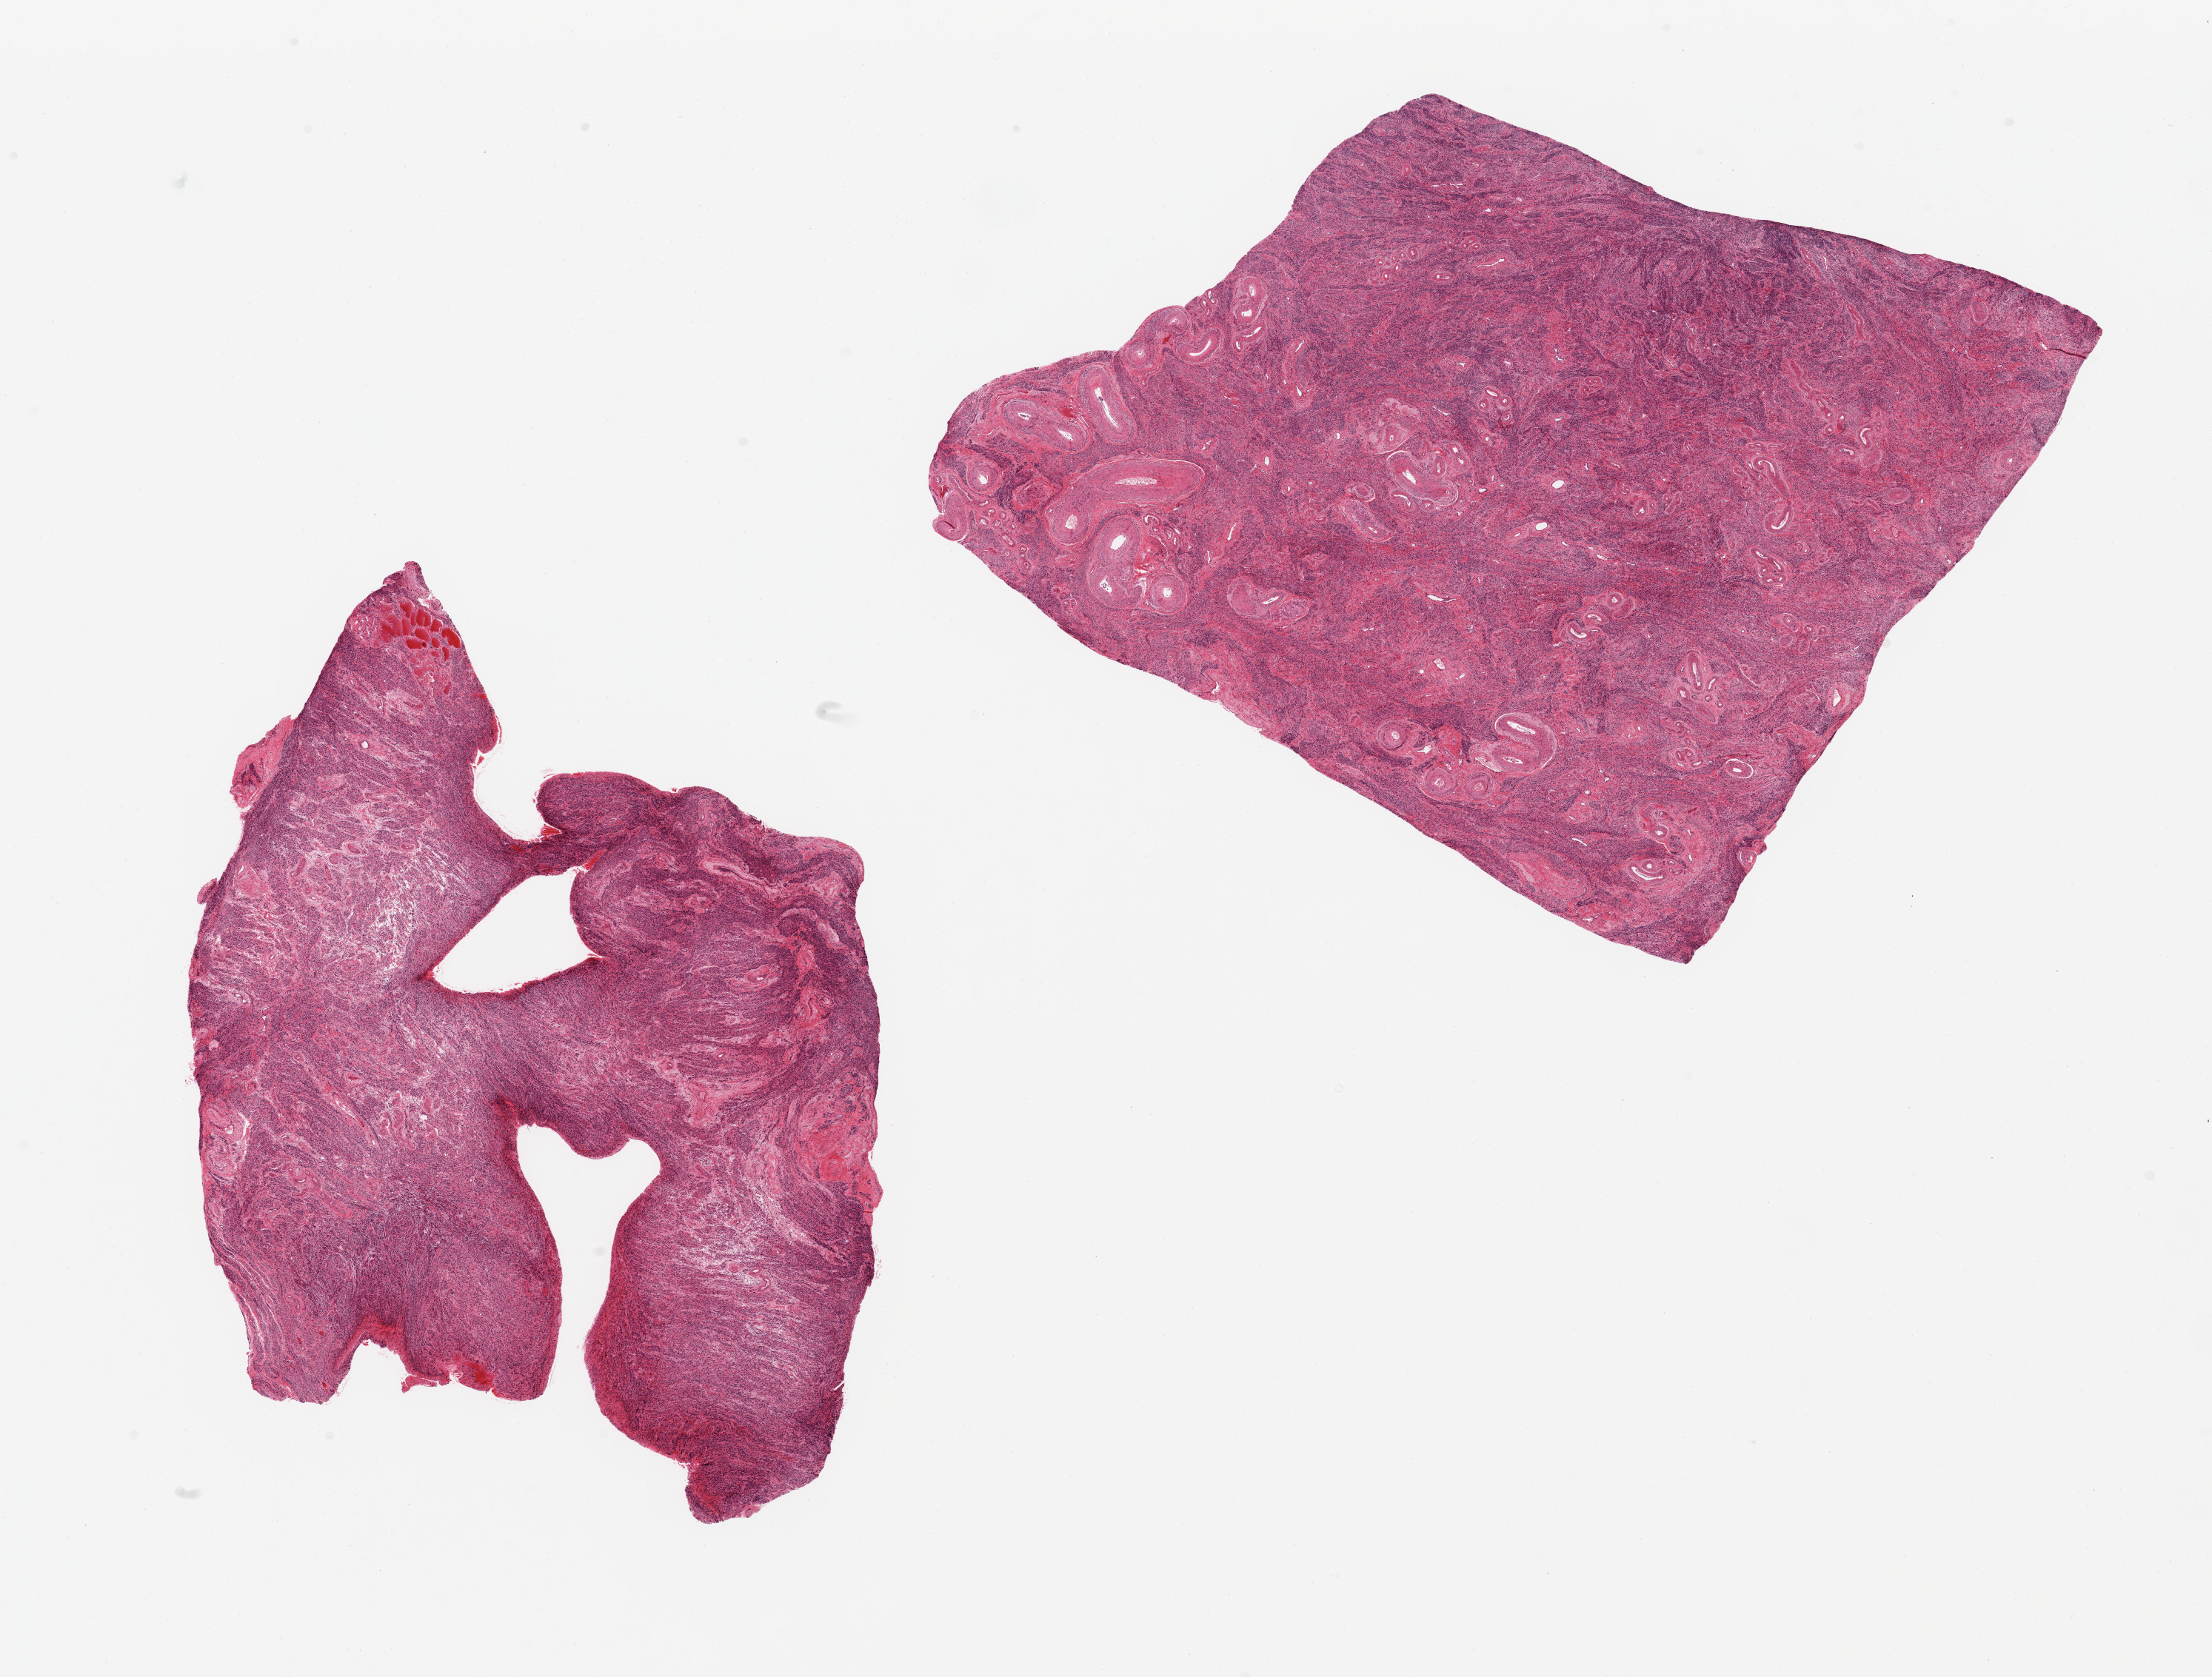
Whole-slide image, haematoxylin and eosin stain, shown as a low-resolution overview of the whole scanned area (about 23.6 x 17.9 mm, slide scanned at 20x). PAXgene-fixed paraffin-embedded (PFPE) section. Section of uterus (target tissue). Donor tissue sample. Donor sex: female.
* review note (as recorded): 2 pieces; endometrium not included